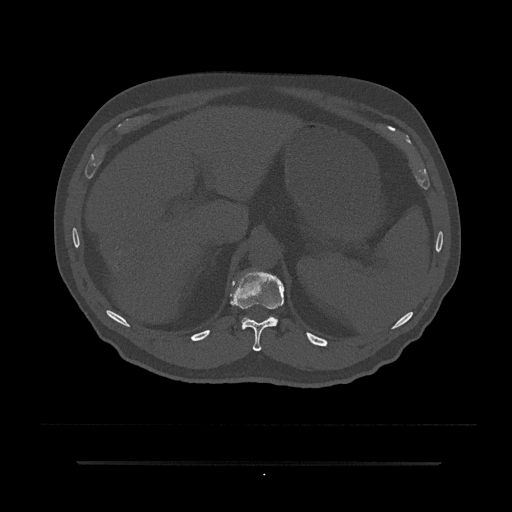
CT including the spine, one axial slice. Position 252 of 797 along the scan axis. Reconstruction kernel Br40s/3. Bone window (W 1800 / L 400 HU). 0.5 mm slice thickness. 512 × 512 image matrix, field of view 464 × 464 mm. Patient: male, 59 years. Case-level facts recorded for this patient, not image findings: primary cancer: bile ducts.
Annotated regions visible in this slice (semi-automatically segmented with operator editing):
- T11 vertebra: bounding box (x1, y1, x2, y2) in pixels: (230, 271, 284, 352)
- T12 vertebra: (241, 316, 277, 327)